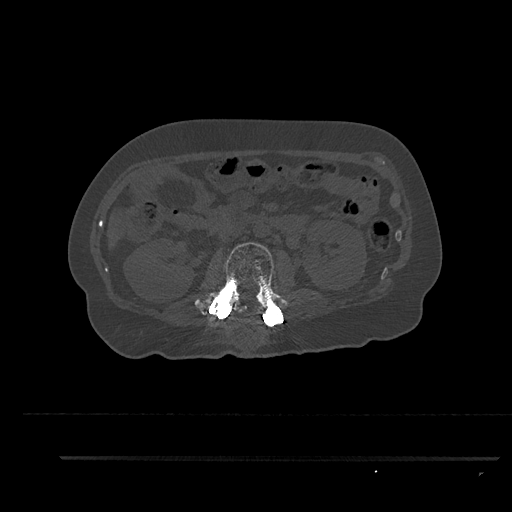
CT including the spine, one axial slice. Position 163 of 797 along the scan axis. Reconstruction kernel Br40s/3. 120 kVp. Bone window (W 1800 / L 400 HU). 0.5 mm slice thickness. 512 × 512 image matrix, field of view 408 × 408 mm. Patient: female, 44 years. From the clinical record (not read from this slice): primary cancer: renal; vertebrae with lytic lesions (as recorded): L1.
Structures marked on this image (semi-automatically segmented with operator editing):
- L2 vertebra: box from (x=195, y=242) to (x=285, y=320) px